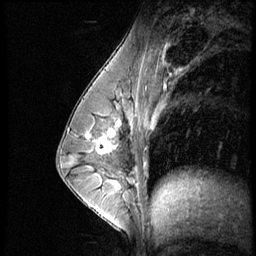
Breast MRI (dynamic contrast-enhanced), one sagittal slice. Slice 31 of 56 in the series (ordered by position). Dynamic contrast-enhanced series, image 2 of 4 at this slice position (ordered by acquisition). 1.5 T. TE 4.2 ms, TR 8.9 ms. 2.5 mm slice thickness. 256 × 256 image matrix, field of view 200 × 200 mm. Patient: female, 35 years. From the clinical record (not read from this slice): setting: breast cancer imaged before/during neoadjuvant chemotherapy; receptor status: HER2-positive.
Annotated regions visible in this slice (semi-automatic segmentation, software-assisted and operator-edited):
- analysis volume of interest (the breast-tissue region the enhancement analysis was run in; not a lesion): bounding box <73,111,131,164> (left, top, right, bottom; pixels)
- tumour enhancement mask (voxels above the 140 % enhancement threshold inside the analysis volume of interest): <88,119,122,154>